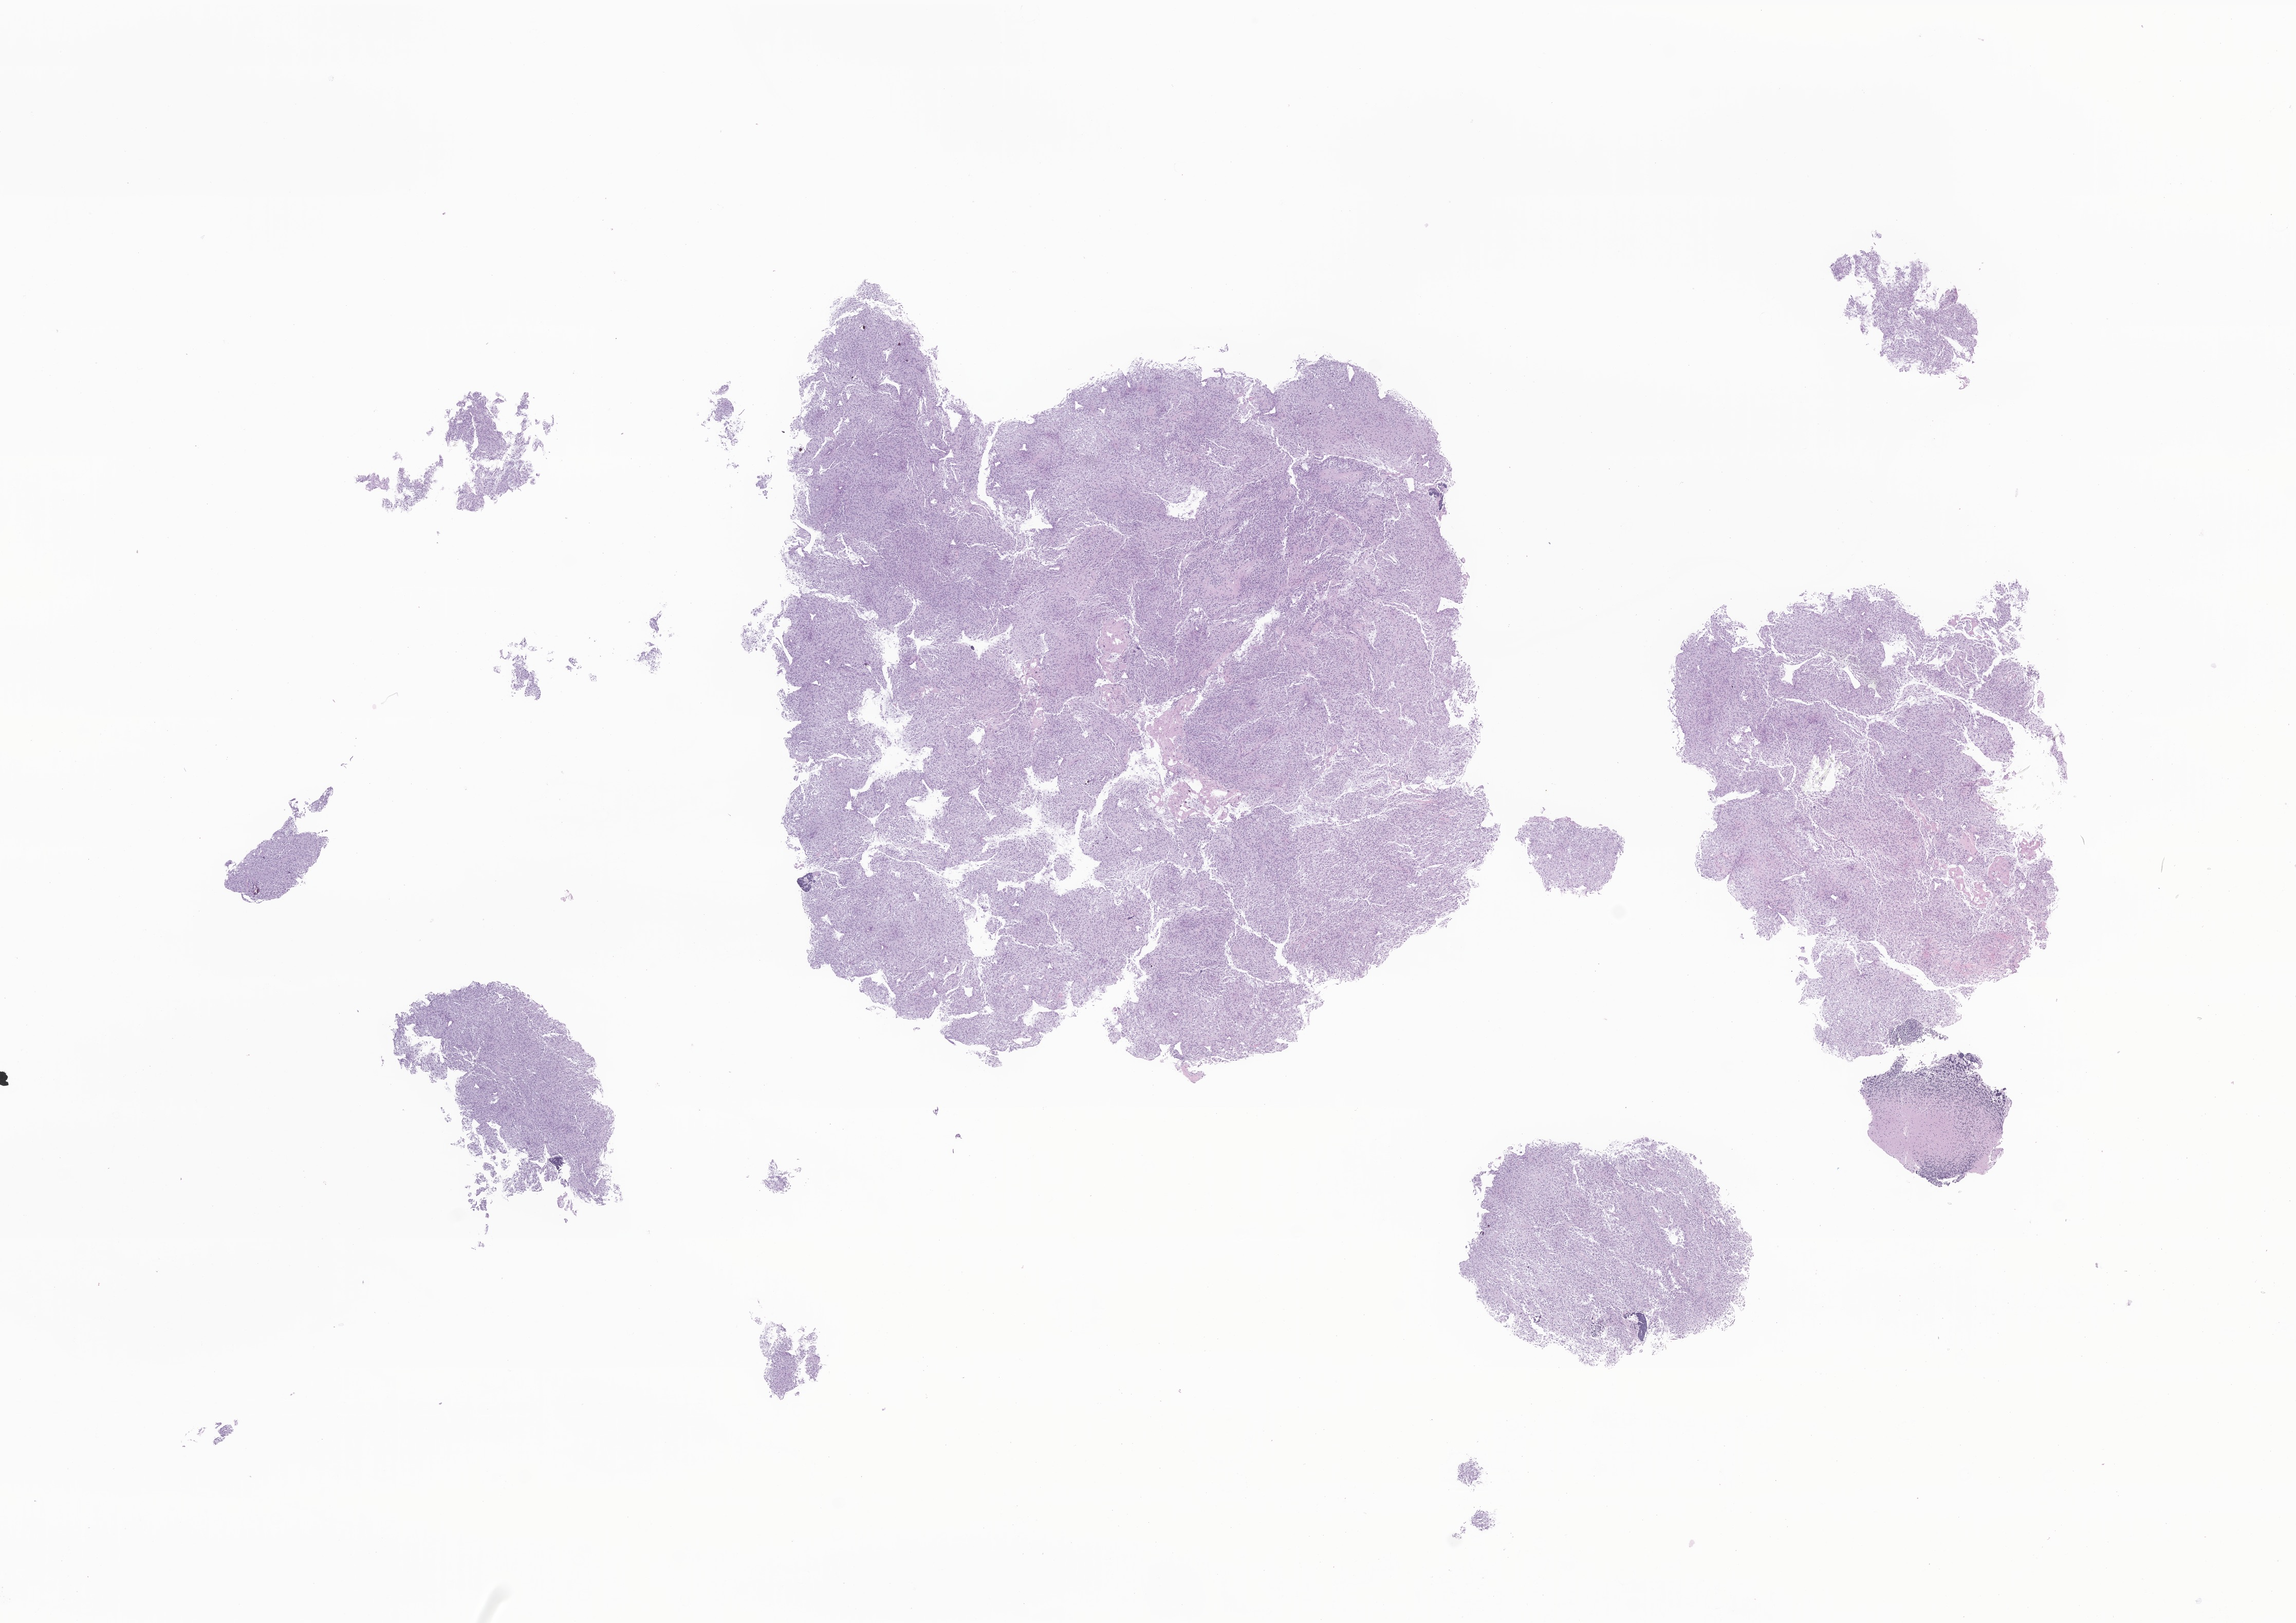
Digitized haematoxylin and eosin-stained section of tumor tissue from the brain stem, shown as a low-resolution overview of the whole scanned area (about 18.8 x 13.3 mm), formalin-fixed paraffin-embedded section. Patient: male, age 119 months (9 years 11 months).
* diagnosis: Pilocytic astrocytoma